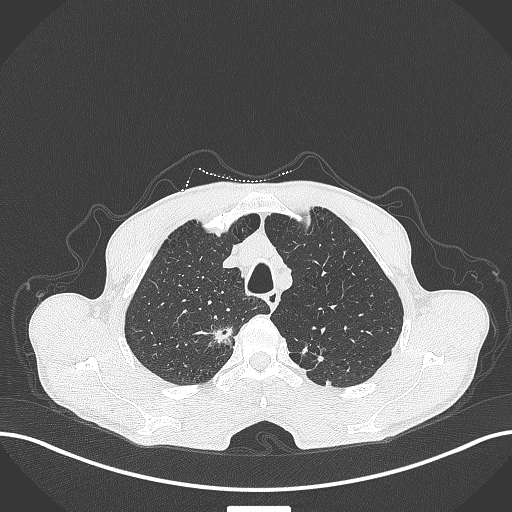
Chest CT, one axial slice; position 352 of 445 along the scan axis; 120 kVp; lung window (W 1500 / L -600 HU); 1 mm slice thickness; 512 × 512 image matrix, field of view 400 × 400 mm. Male patient, age 70 years. From the clinical record (not read from this slice): clinical TNM (as recorded): T1a N0 M0.
Outlined on this slice (bounding box drawn by a radiologist):
- lung tumour (recorded histology: adenocarcinoma): box from (x=209, y=322) to (x=237, y=349) px